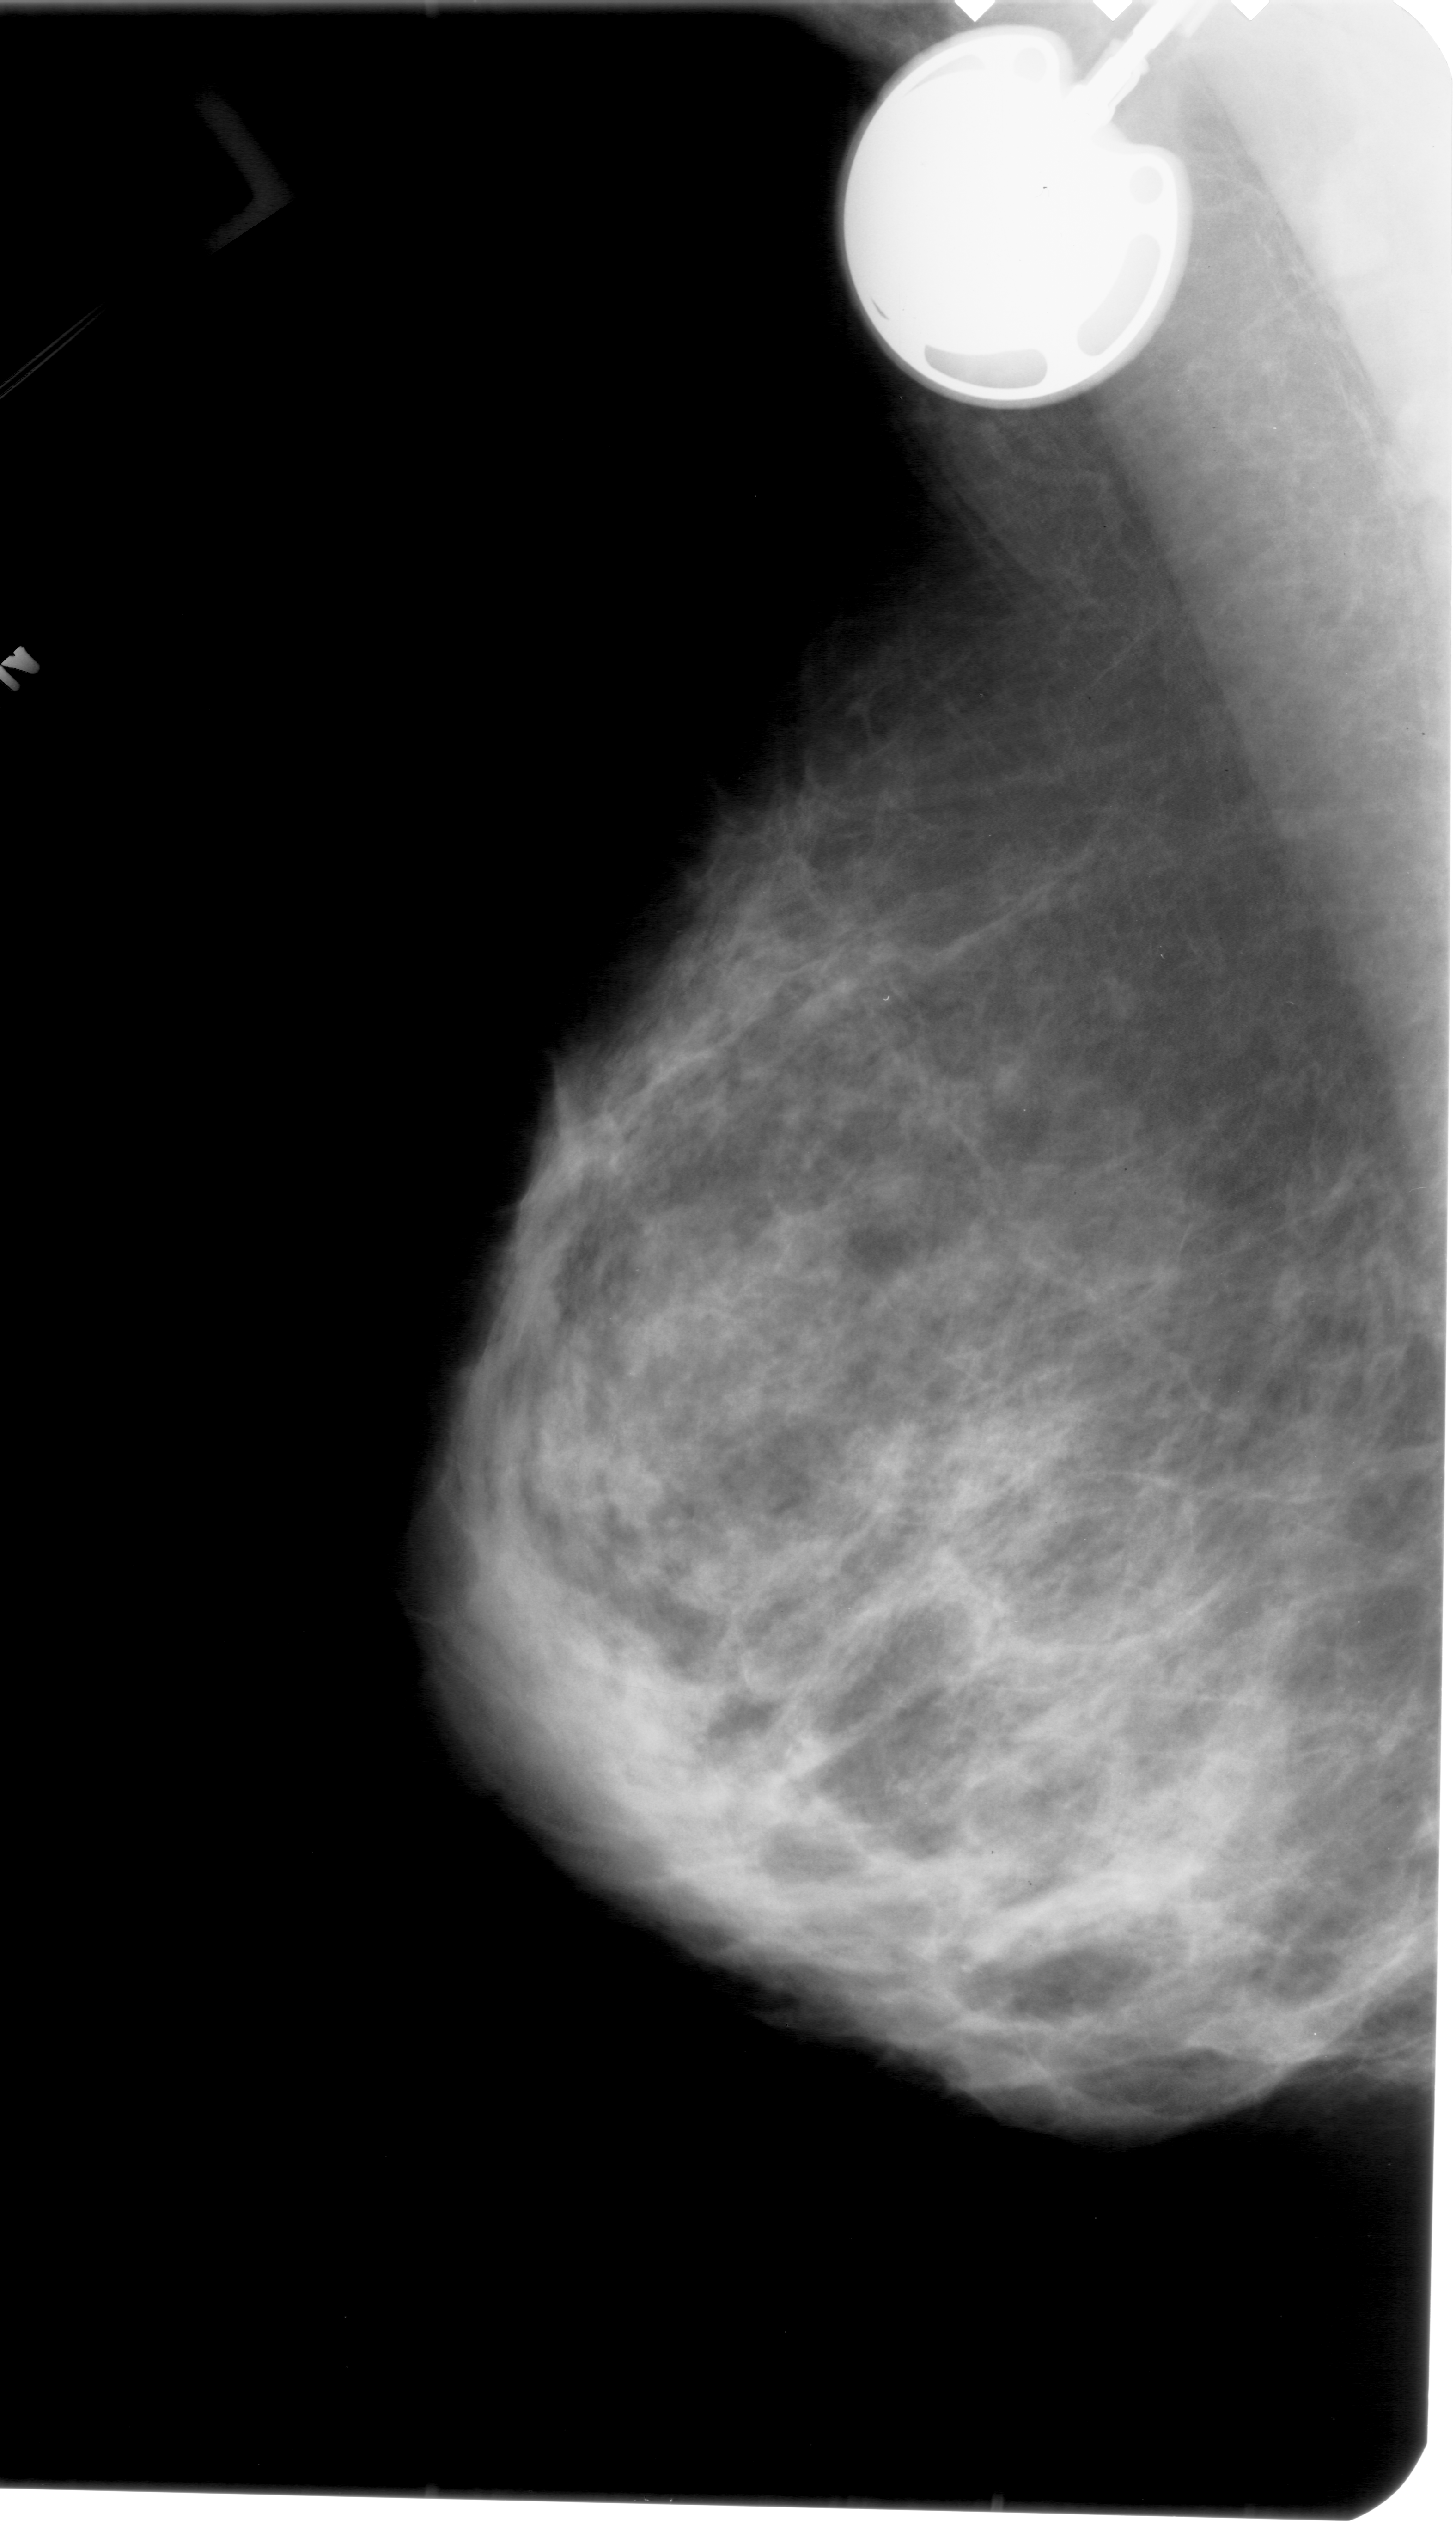
Scanned film-screen mammogram, left breast, mediolateral oblique (MLO) view, BI-RADS breast density category 3 (scale 1–4).
Calcifications, morphology fine linear branching, distribution linear; BI-RADS assessment category 4; subtlety rating 1 on a 1 (subtle) to 5 (obvious) scale; pathology result (as recorded, not read from the image): malignant.